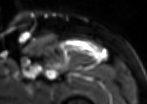
MRI of an extremity soft-tissue mass, one axial slice; position 78 of 85 along the scan axis; T2-weighted fat-saturated; MR volume resampled by the dataset authors to the PET/CT grid (not the native acquisition matrix); 3.27 mm slice thickness; 147 × 104 image matrix, field of view 144 × 102 mm. Male patient. From the clinical record (not read from this slice): histological type: extraskeletal osteosarcoma; grade: high; site of the primary tumour: thigh.
Outlined on this slice (expert contour drawn on MRI and transferred to this co-registered scan by the dataset authors):
- gross tumour volume (mass): bounding box (x1, y1, x2, y2) in pixels: (65, 39, 105, 59)